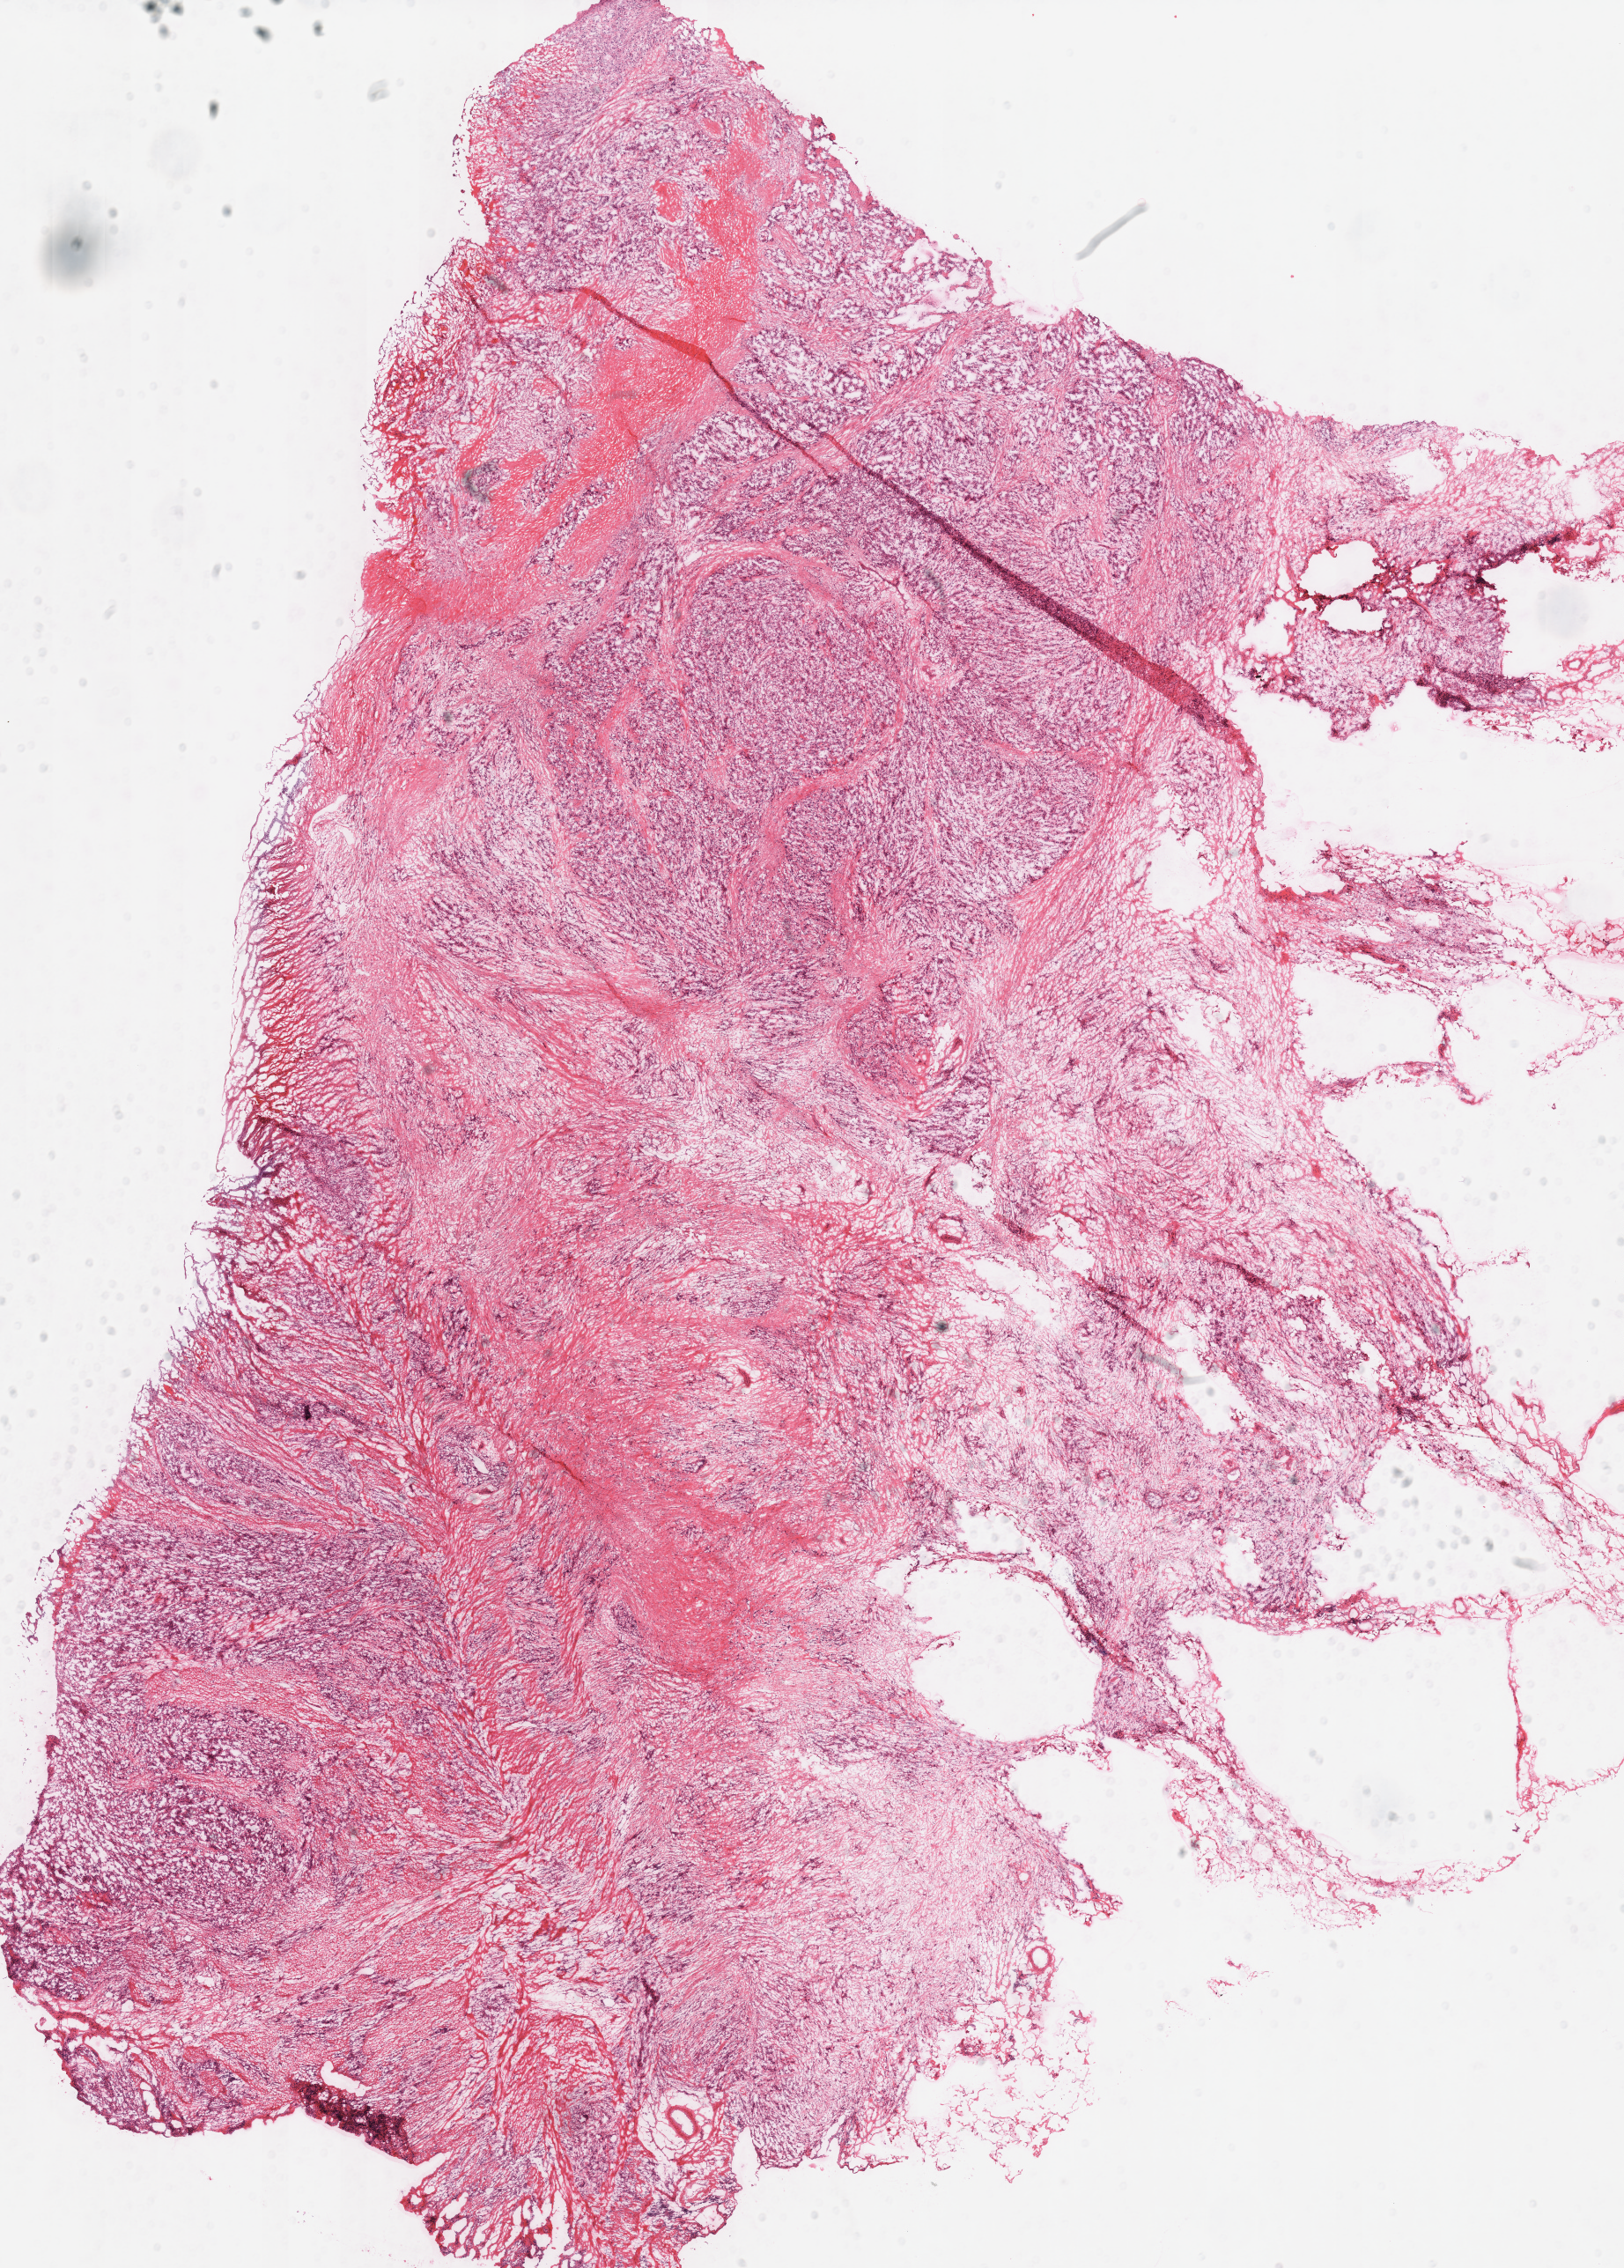
Digitized H&E tissue section (whole slide) — shown as a low-resolution overview of the whole scanned area (about 14.5 x 20.3 mm, from a 40x scan). Frozen section from the top of the tissue portion. Stomach, primary tumour sample. Patient: female, age at initial diagnosis 74 years. Histologic grade: G3 (poorly differentiated). Composition of this section per pathologist review: tumour cells 72%, tumour nuclei 61%, normal cells 0%, stromal cells 28%, necrosis 0%. Infiltration values recorded for this section: lymphocyte infiltration 20%, monocyte infiltration 0%, neutrophil infiltration 10%.
AJCC pathologic stage: IIIB (7th edition). Pathologic diagnosis: Adenocarcinoma, NOS (gastric antrum).